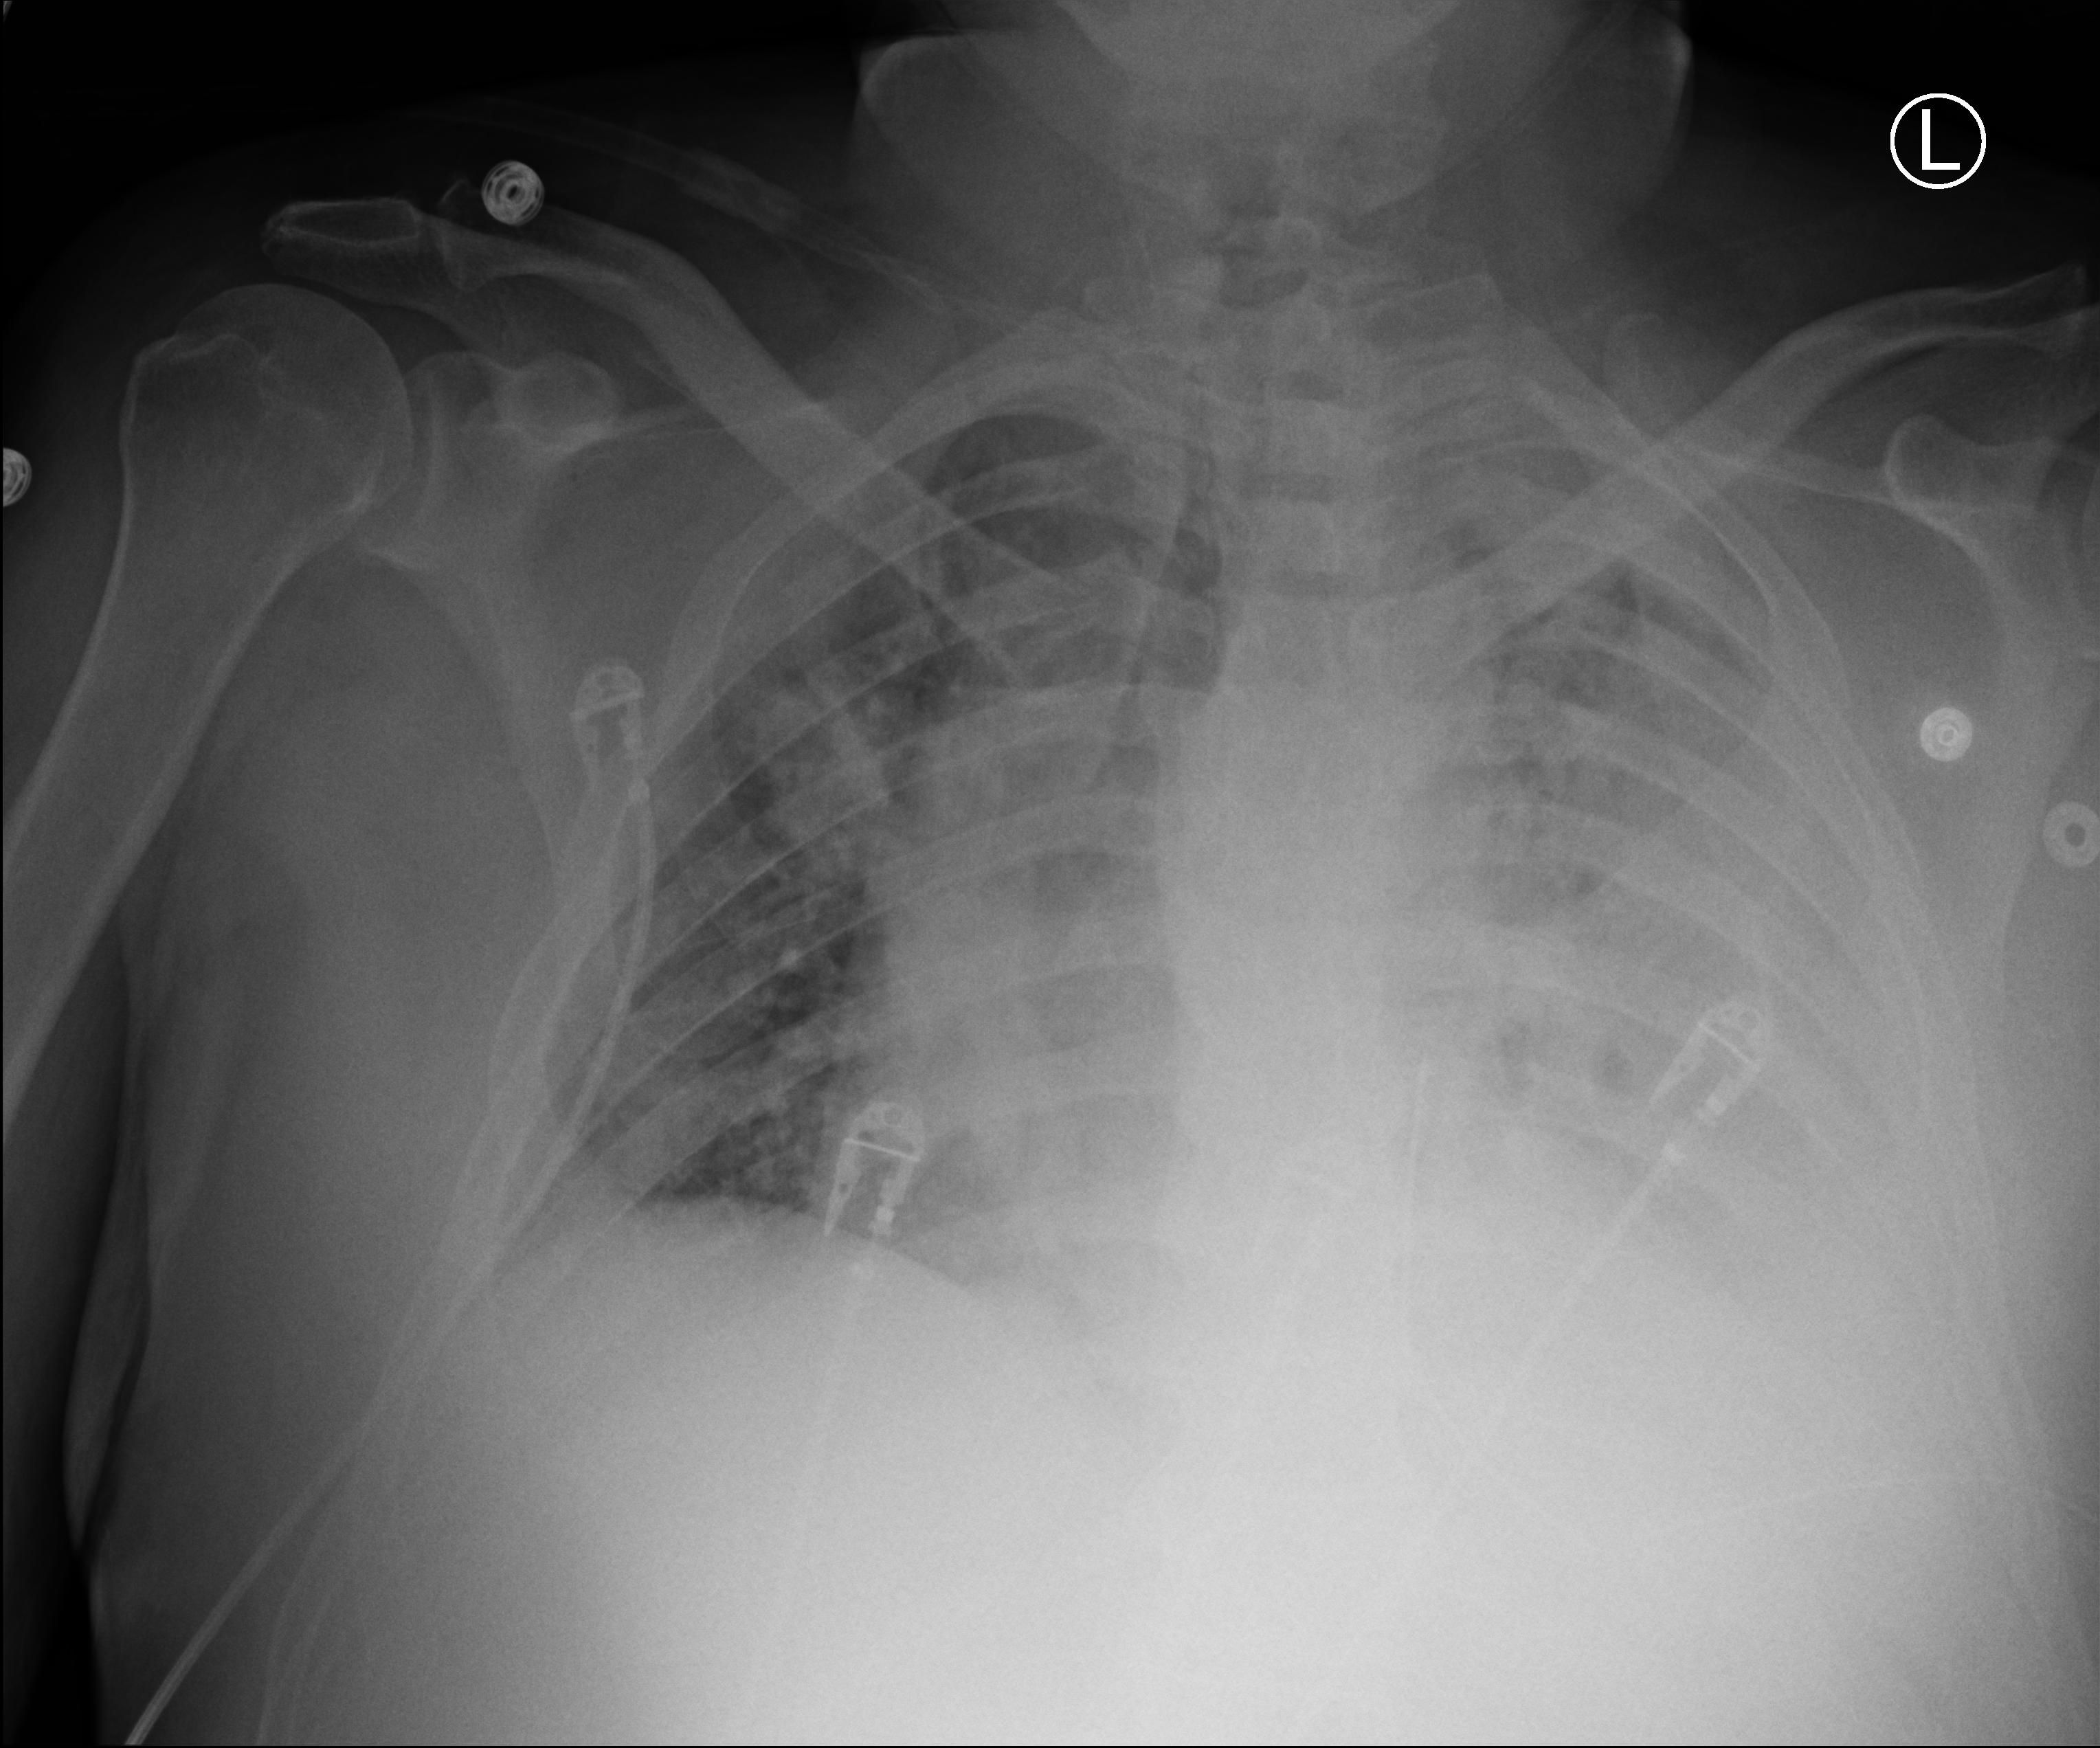
Portable chest radiograph, anteroposterior (AP) projection. Patient hospitalised with COVID-19; male, aged 18–59 years.
Hospital-stay facts (about this admission, not read from this image; timing relative to this image not recorded): admitted to intensive care during this hospital stay: no; mechanically ventilated during this hospital stay: no; length of hospital stay: 10 days.